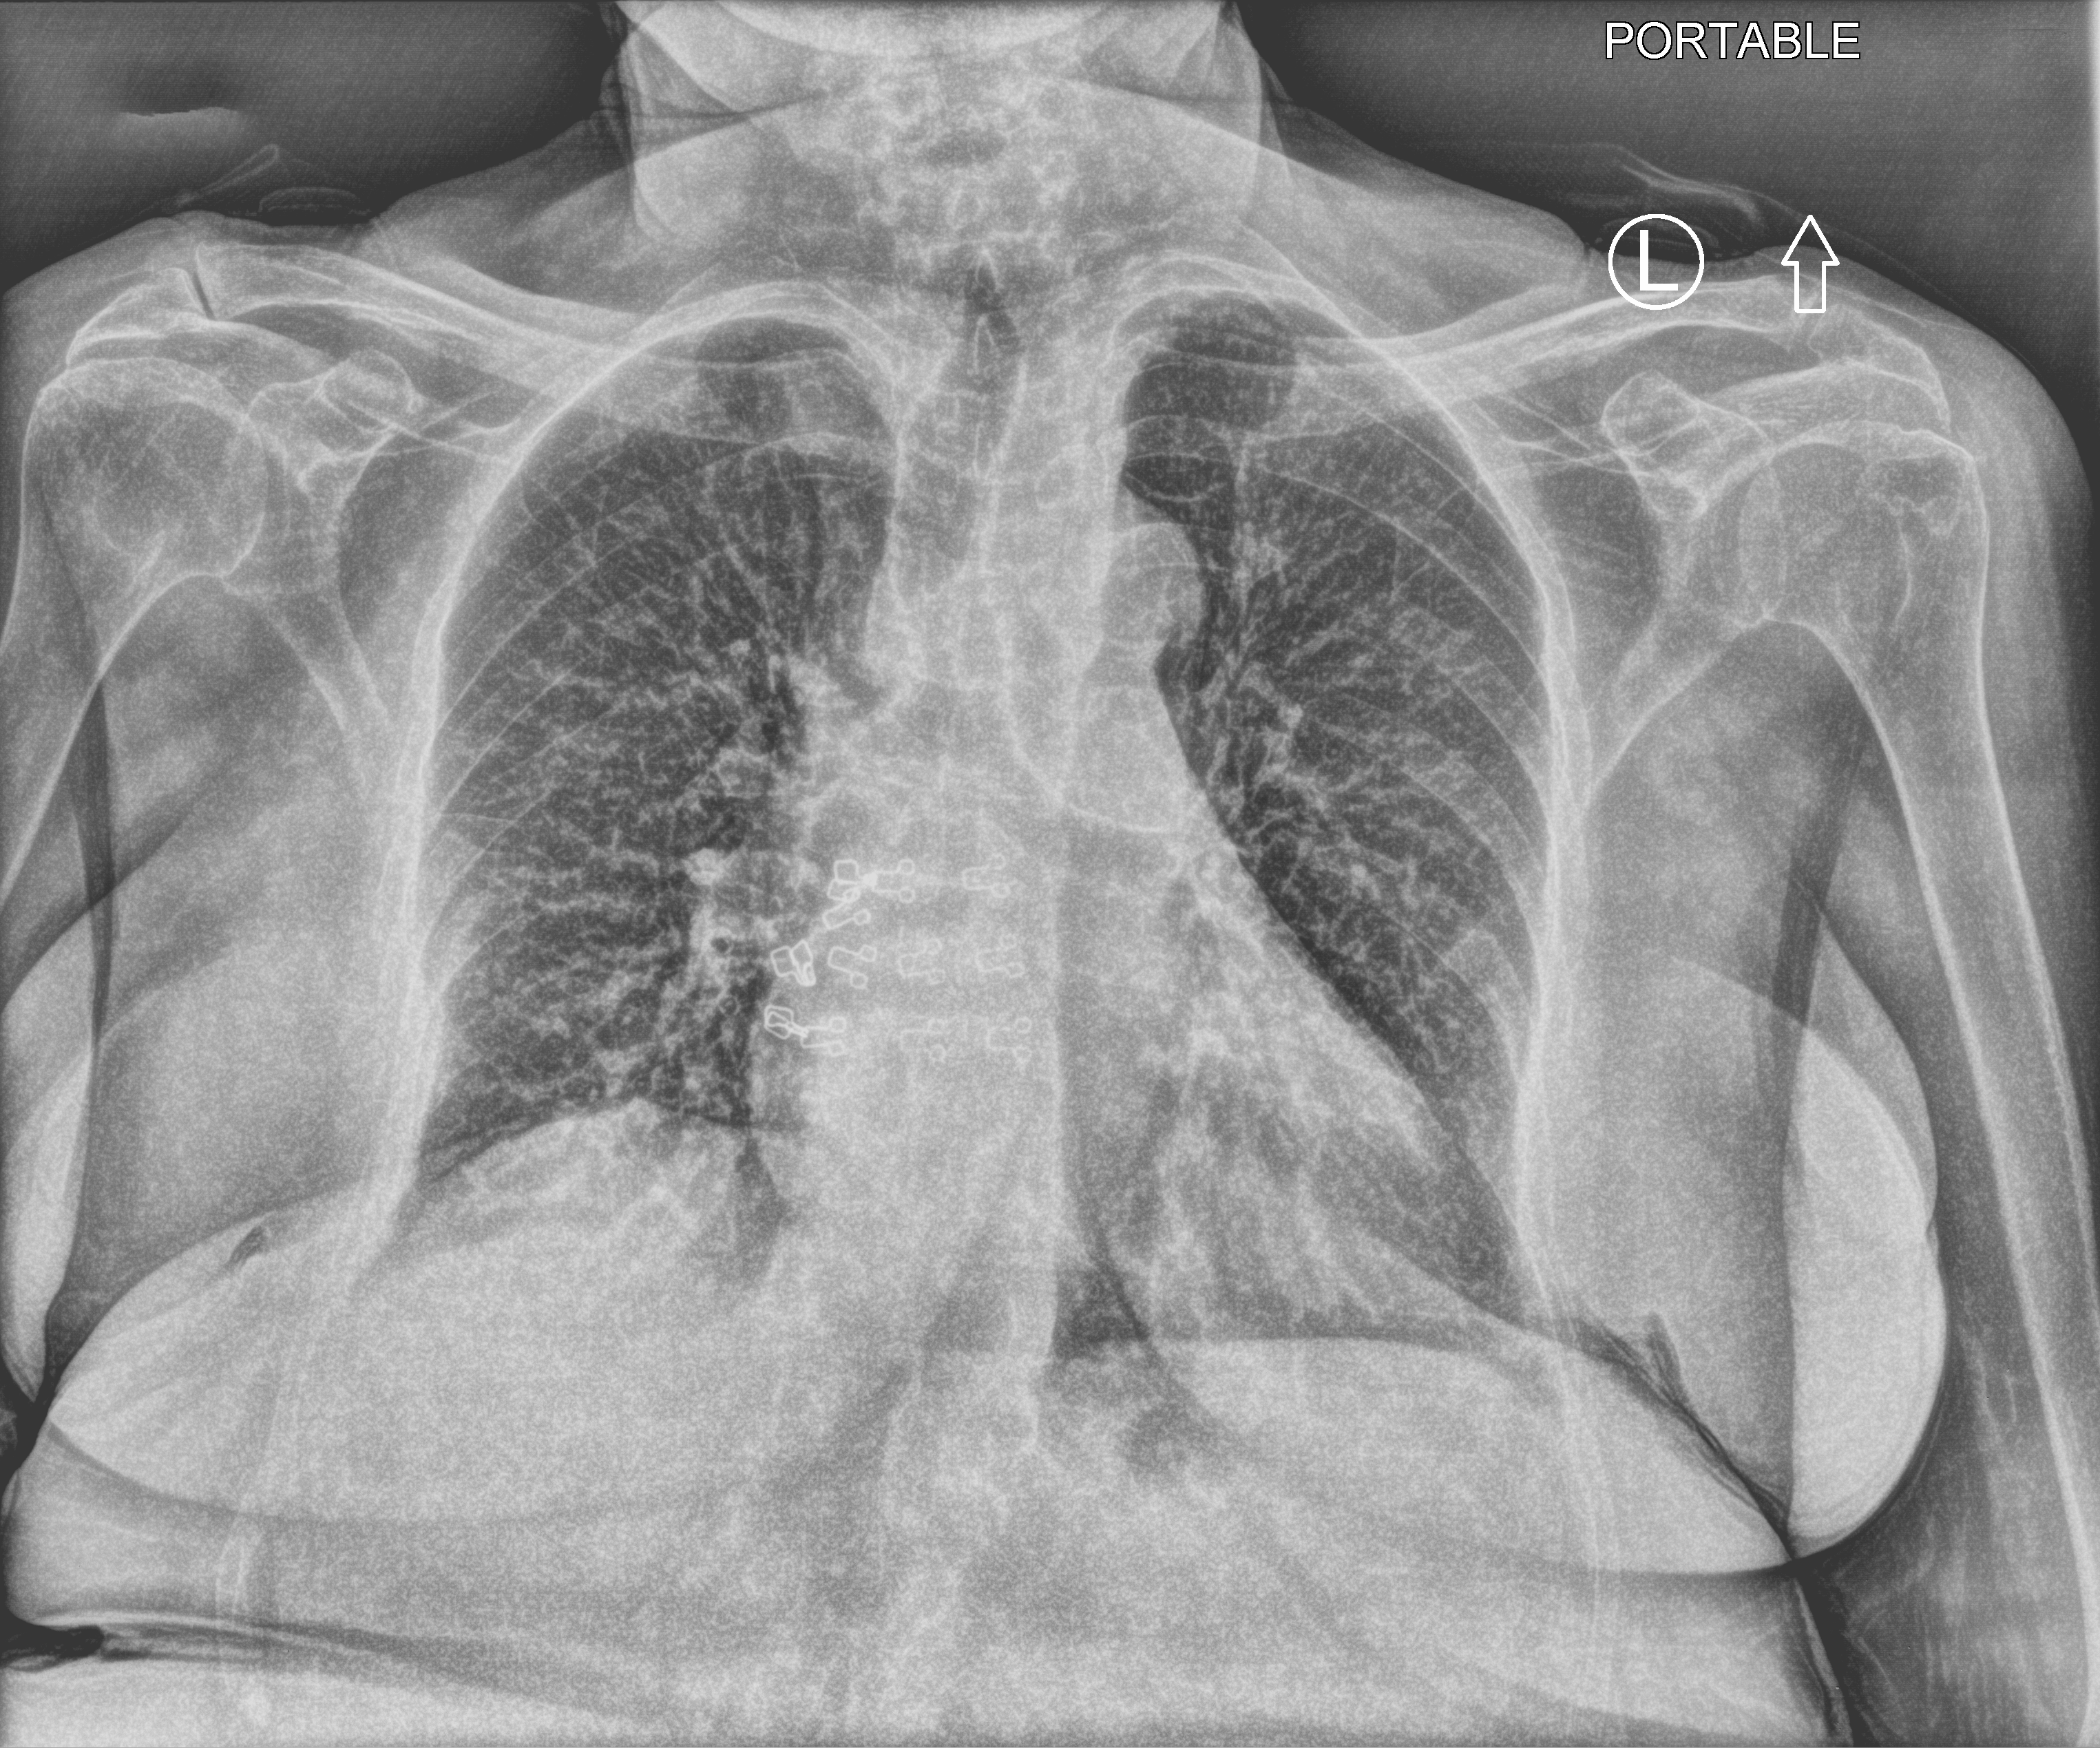
Bedside chest radiograph (computed radiography). Patient hospitalised with COVID-19; female, aged 75–90 years.
From the hospital-stay record, not from the radiograph (when in the stay this image was taken is not recorded): mechanically ventilated during this hospital stay: no; admitted to intensive care during this hospital stay: no.